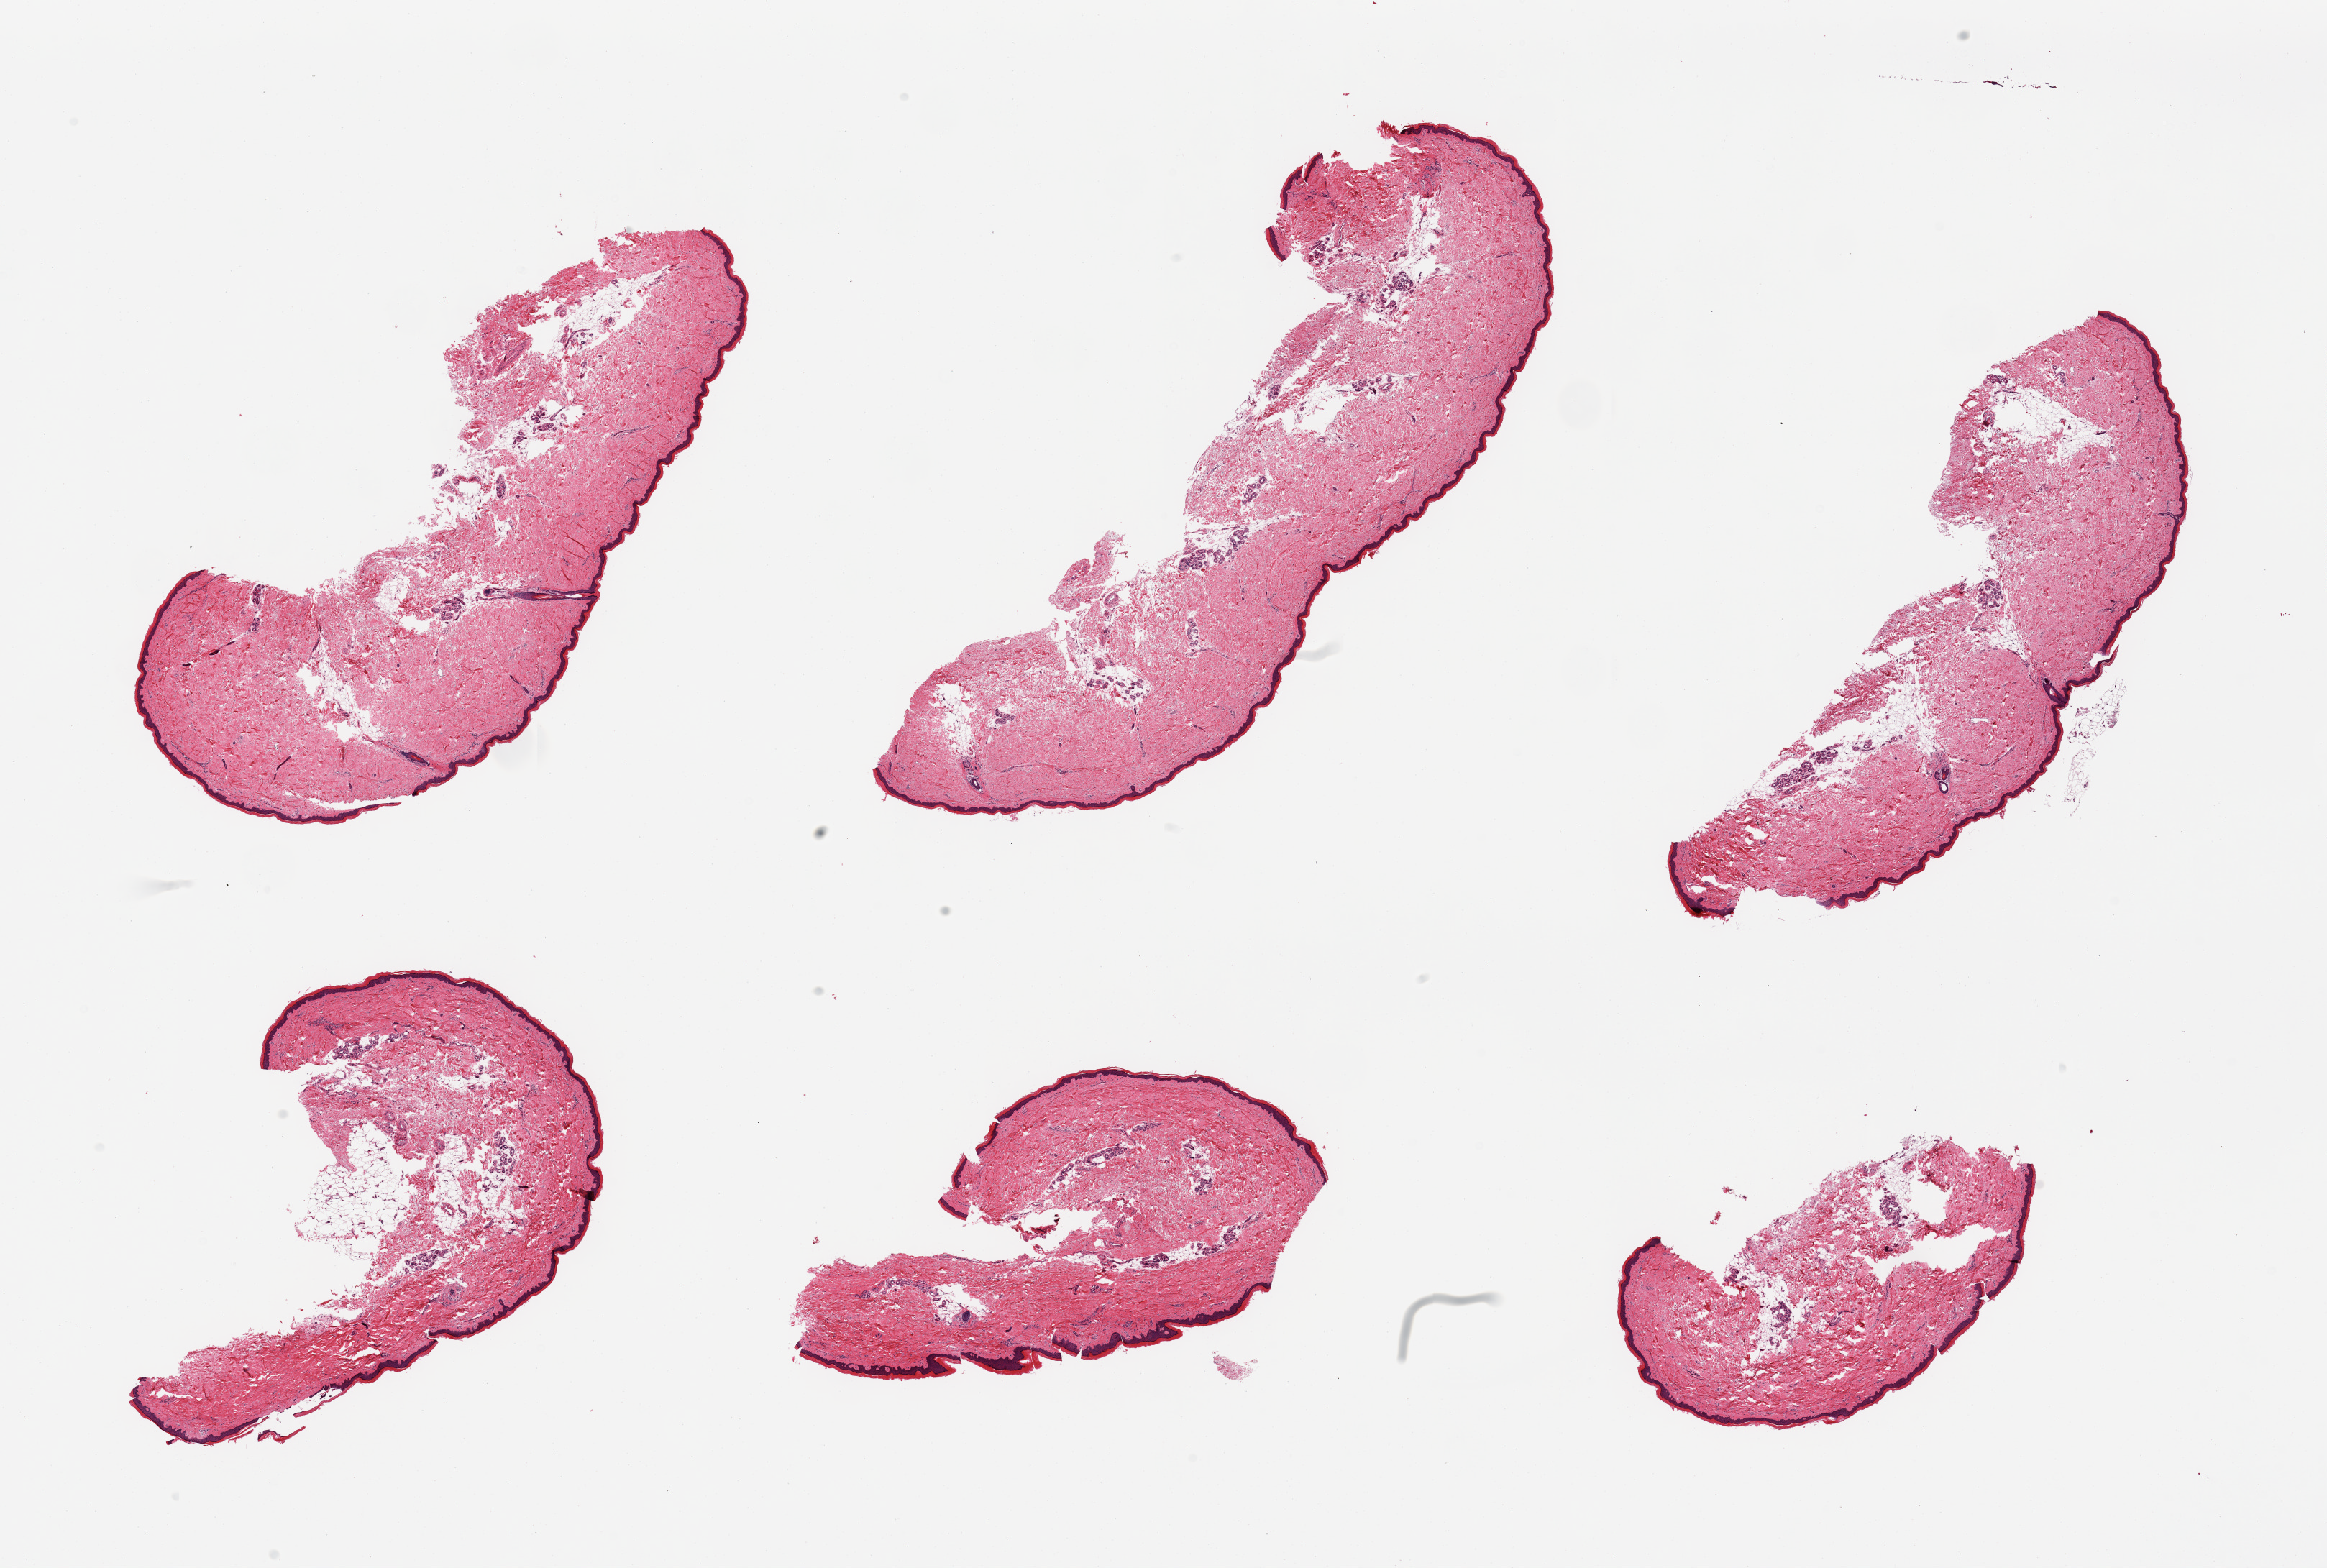
Hematoxylin and eosin (H&E) whole-slide image, brightfield — whole scanned area (about 25.6 x 17.3 mm, from a 20x scan) shown as a low-resolution overview. PAXgene-fixed paraffin-embedded (PFPE) section. Target tissue: skin of lower leg. Donor tissue sample. Donor: female.
• review note (as recorded): 6 pieces; up to 10% attached and internal fat, epidermis measures 35 microns